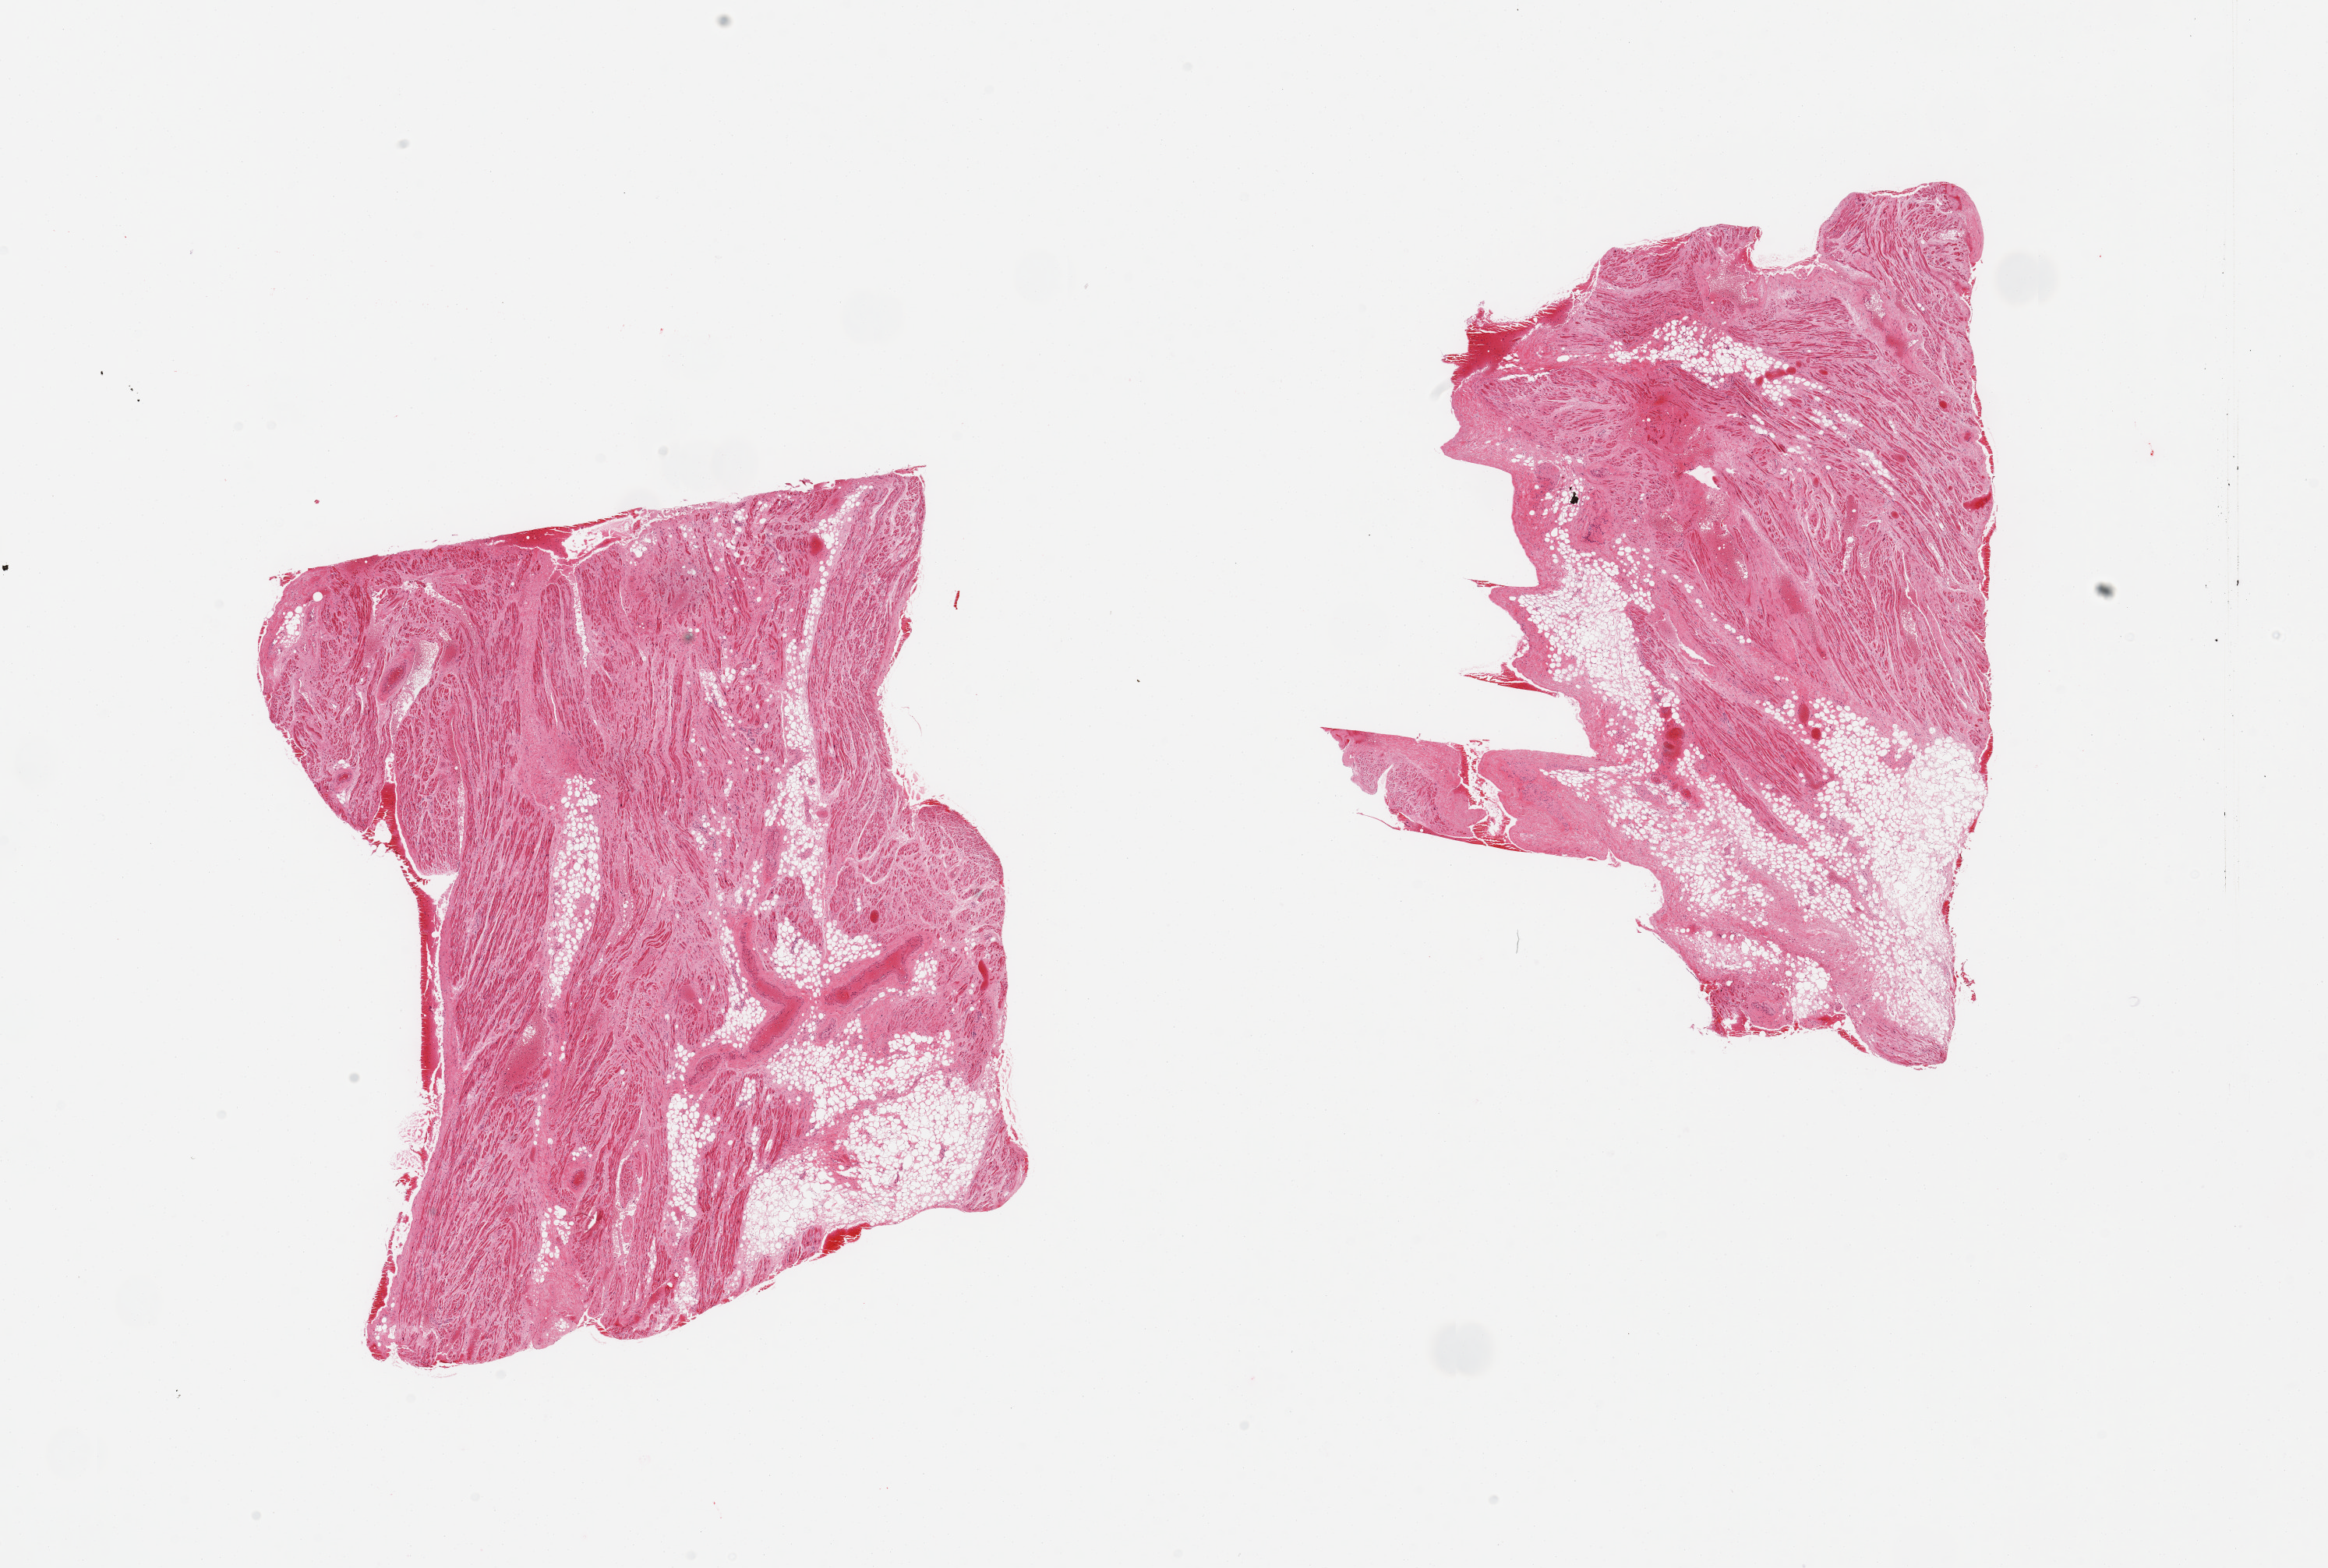
Whole-slide image, hematoxylin and eosin (H&E) stain — whole scanned area (about 23.6 x 15.9 mm, from a 20x scan) shown as a low-resolution overview. PAXgene-fixed paraffin-embedded (PFPE) section. Sampled site (target tissue): auricular appendage. Donor tissue sample. Donor: male.
Pathologist's review note for this sample: 2 pieces; includes 30 and 40% fat/fibrous tissue.